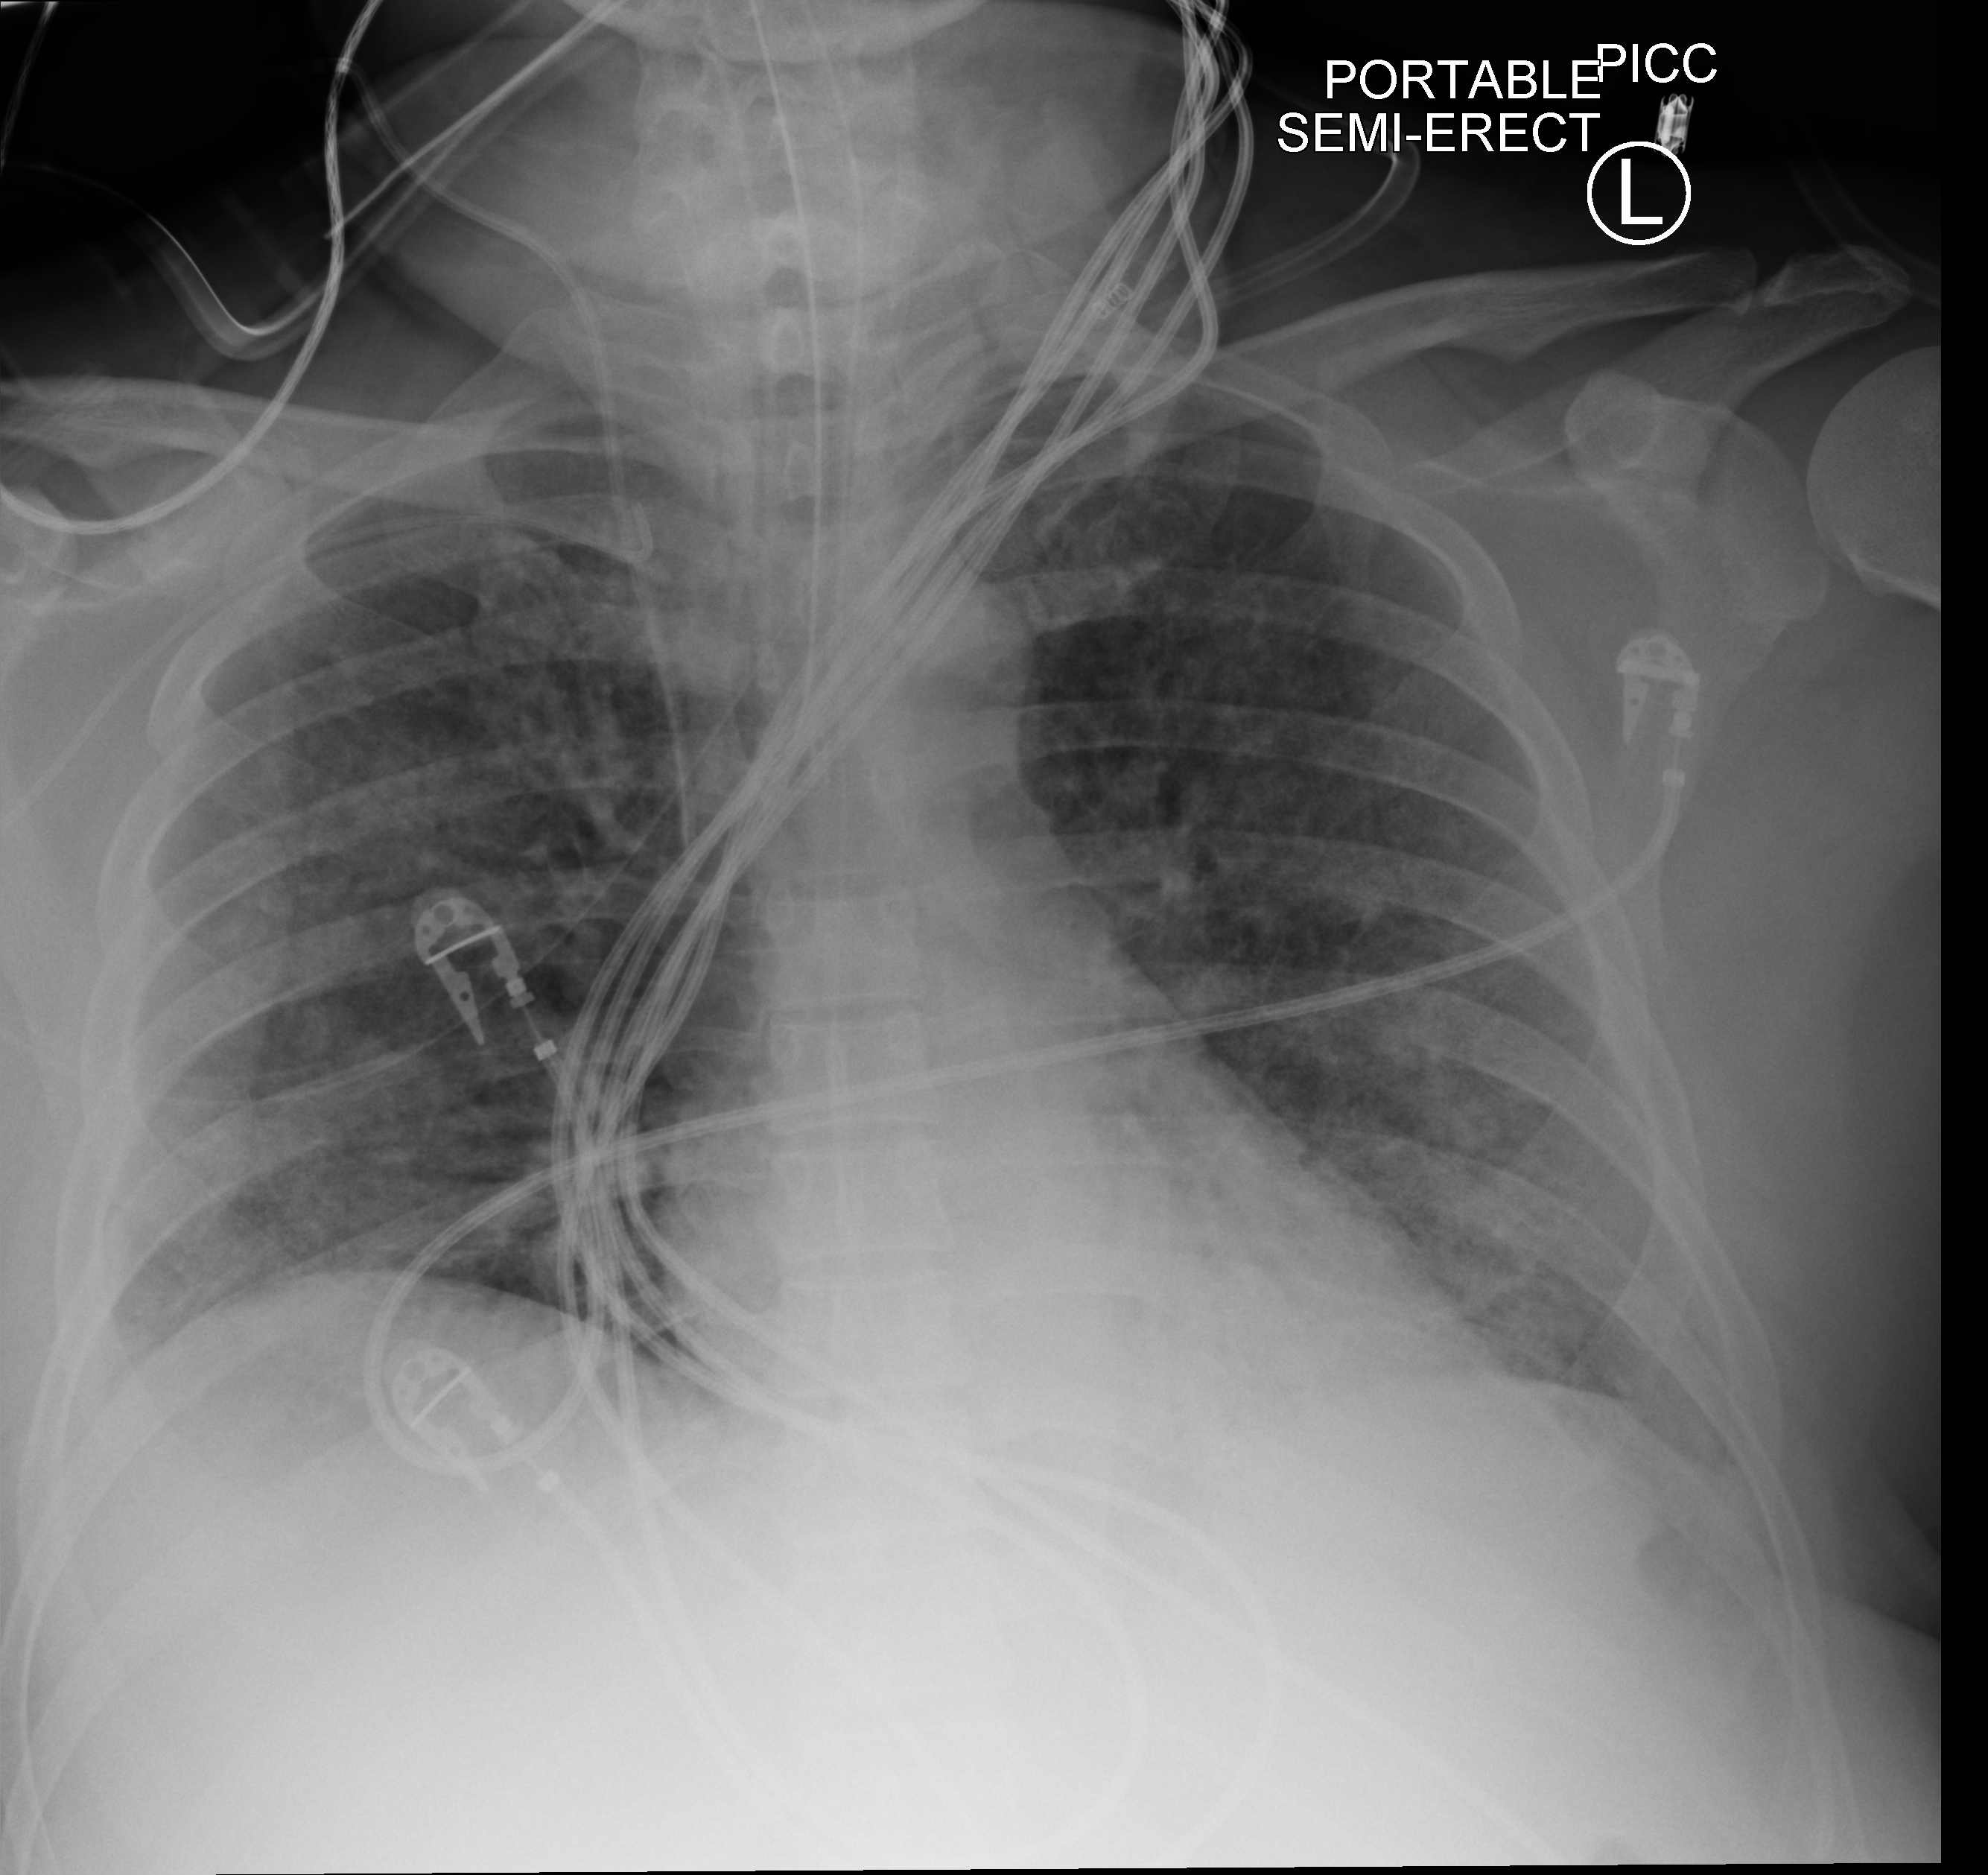
Portable chest radiograph; anteroposterior (AP) projection. Patient hospitalised with COVID-19; male, aged 18–59 years.
From the hospital-stay record, not from the radiograph (when in the stay this image was taken is not recorded):
- hypertension (admission record): no
- mechanically ventilated during this hospital stay: yes